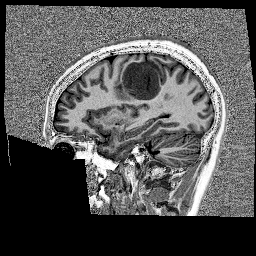
Brain MRI from a brain-tumour surgery series, one sagittal slice; slice 59 of 176 in the series (ordered by position); 256 × 256 image matrix, field of view 256 × 256 mm. From the clinical record (not read from this slice): histopathology: Glioblastoma; WHO grade: 4.
Structures marked on this image (outlined manually by an expert reader):
- tumour: bounding box [x1, y1, x2, y2] px = [118, 58, 175, 105]